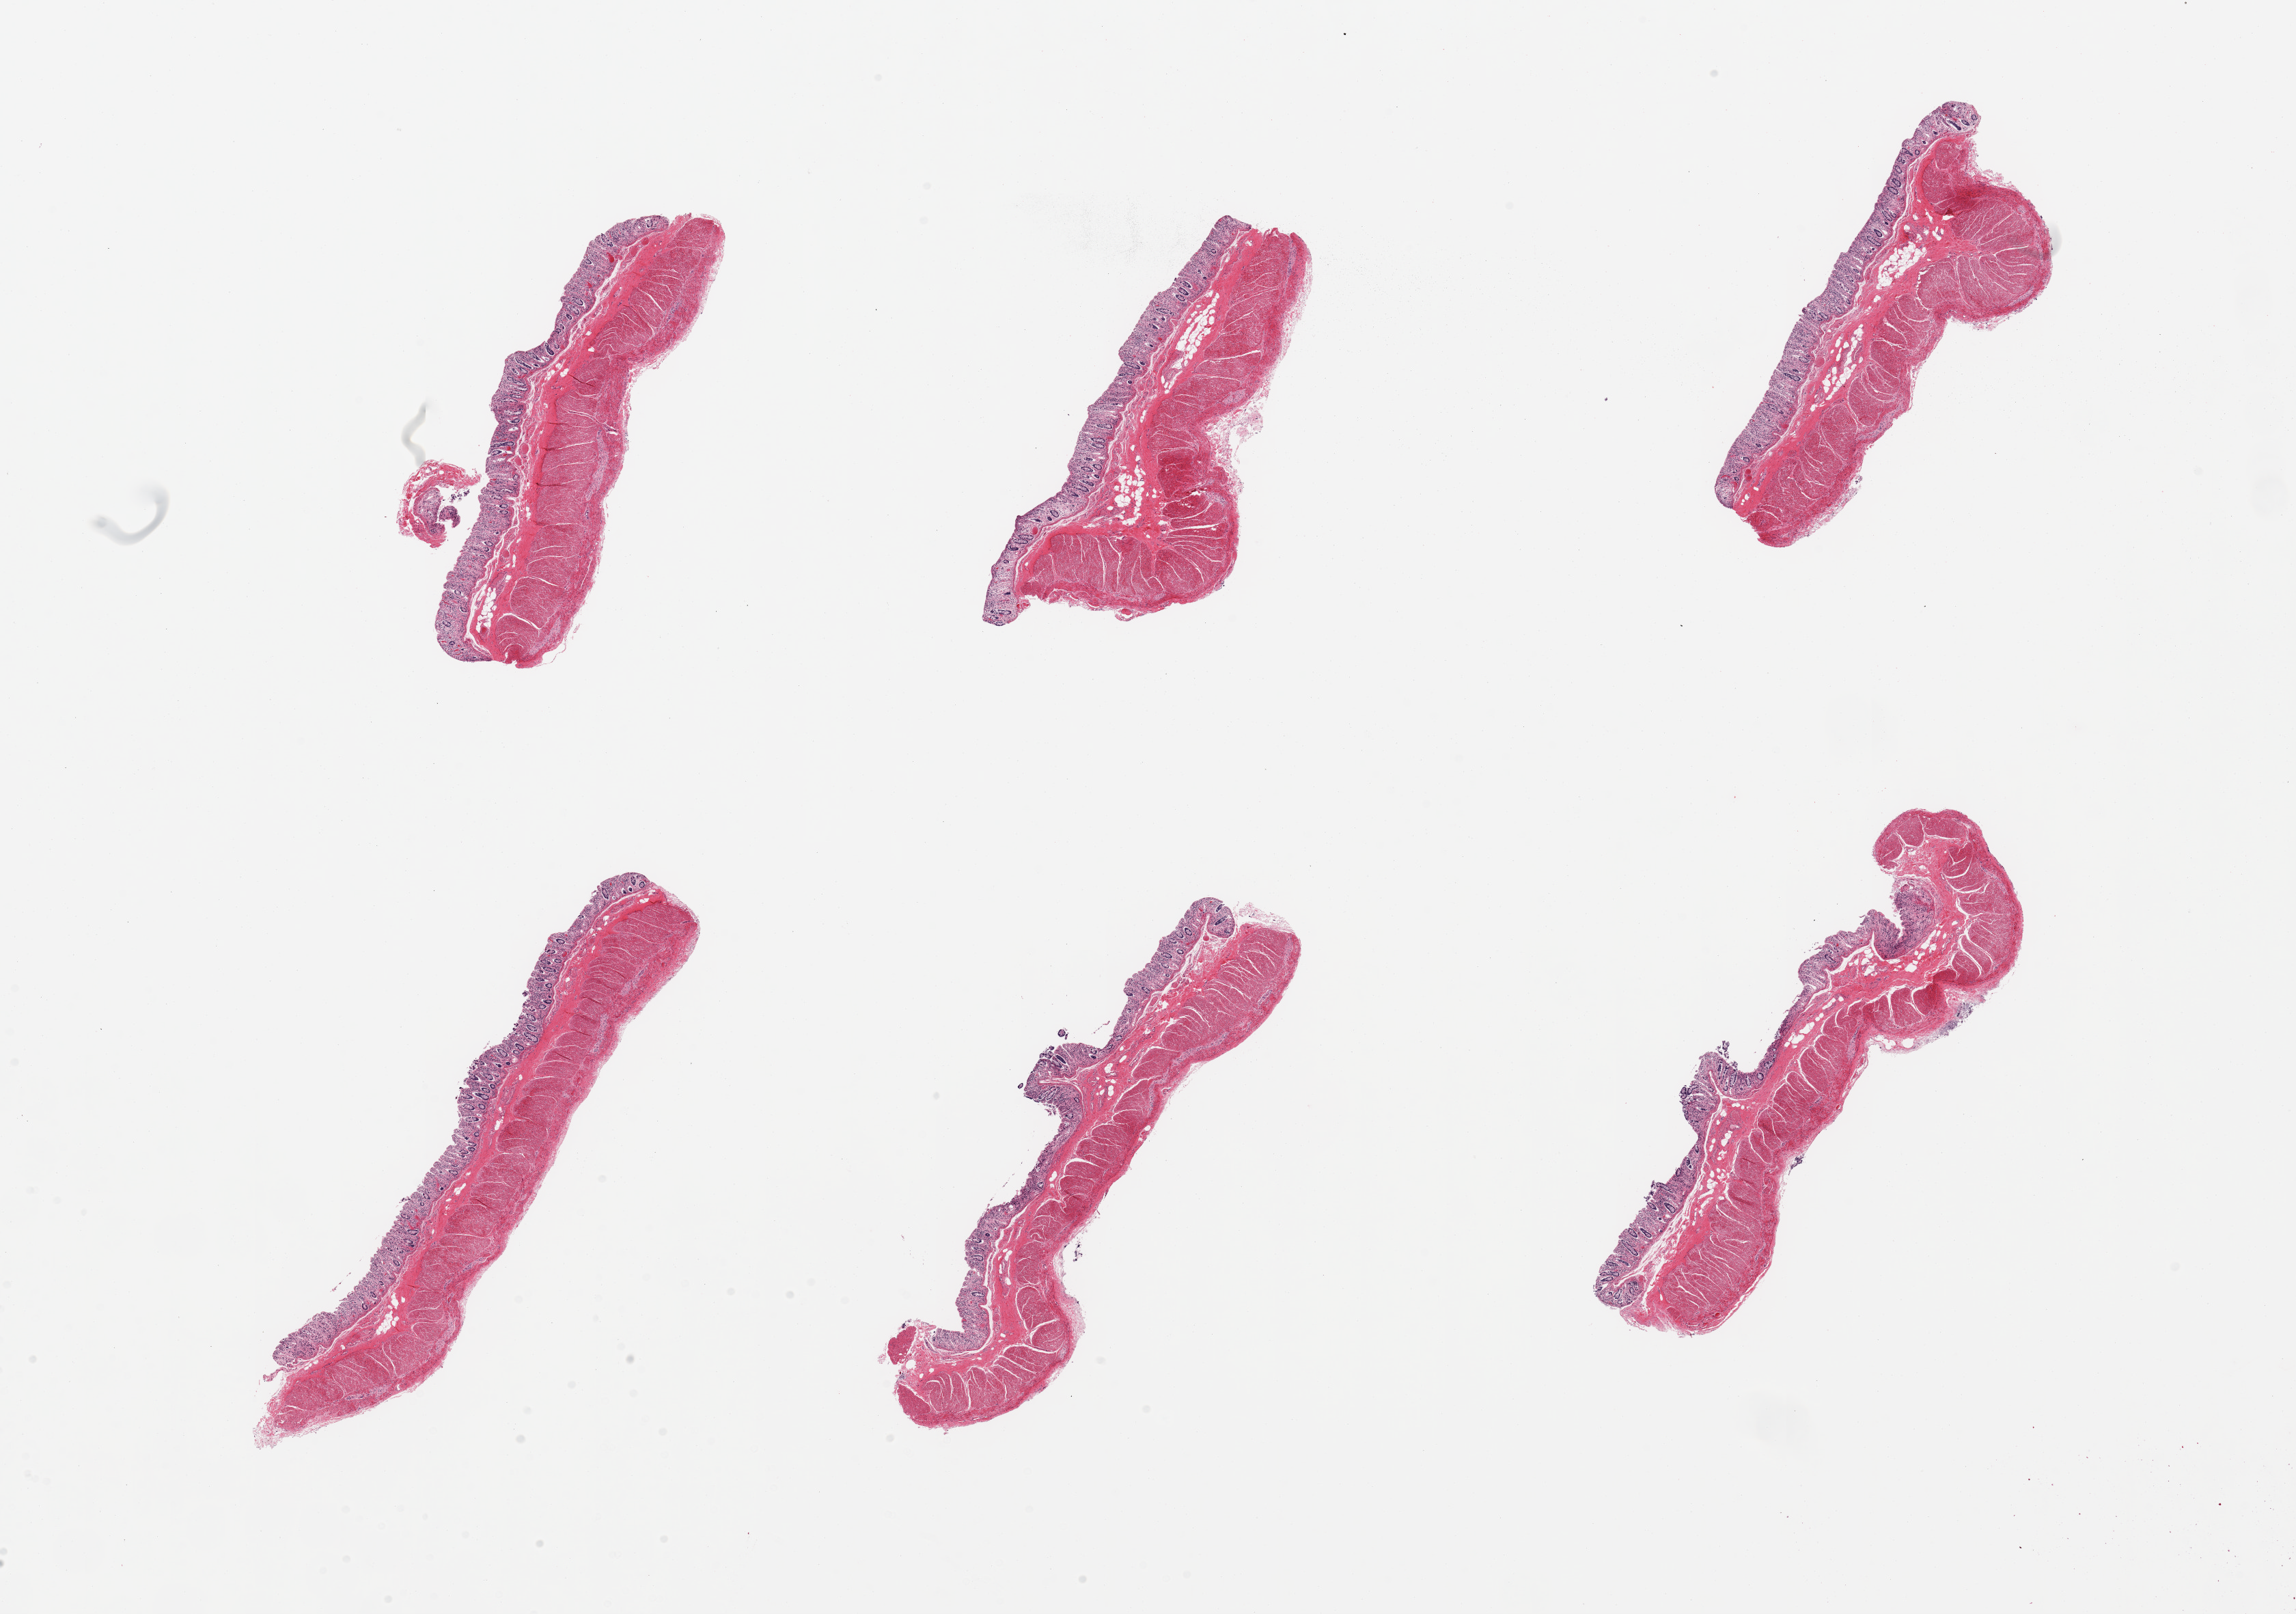
Whole-slide image, hematoxylin and eosin (H&E) stain — whole scanned area (about 26.6 x 18.7 mm) shown as a low-resolution overview; PAXgene-fixed, paraffin-embedded tissue; section of transverse colon (target tissue); tissue donor sample. Donor sex: male.
• pathologist's review note for this sample: 6 pieces; mucosa autolyzed, muscle intact